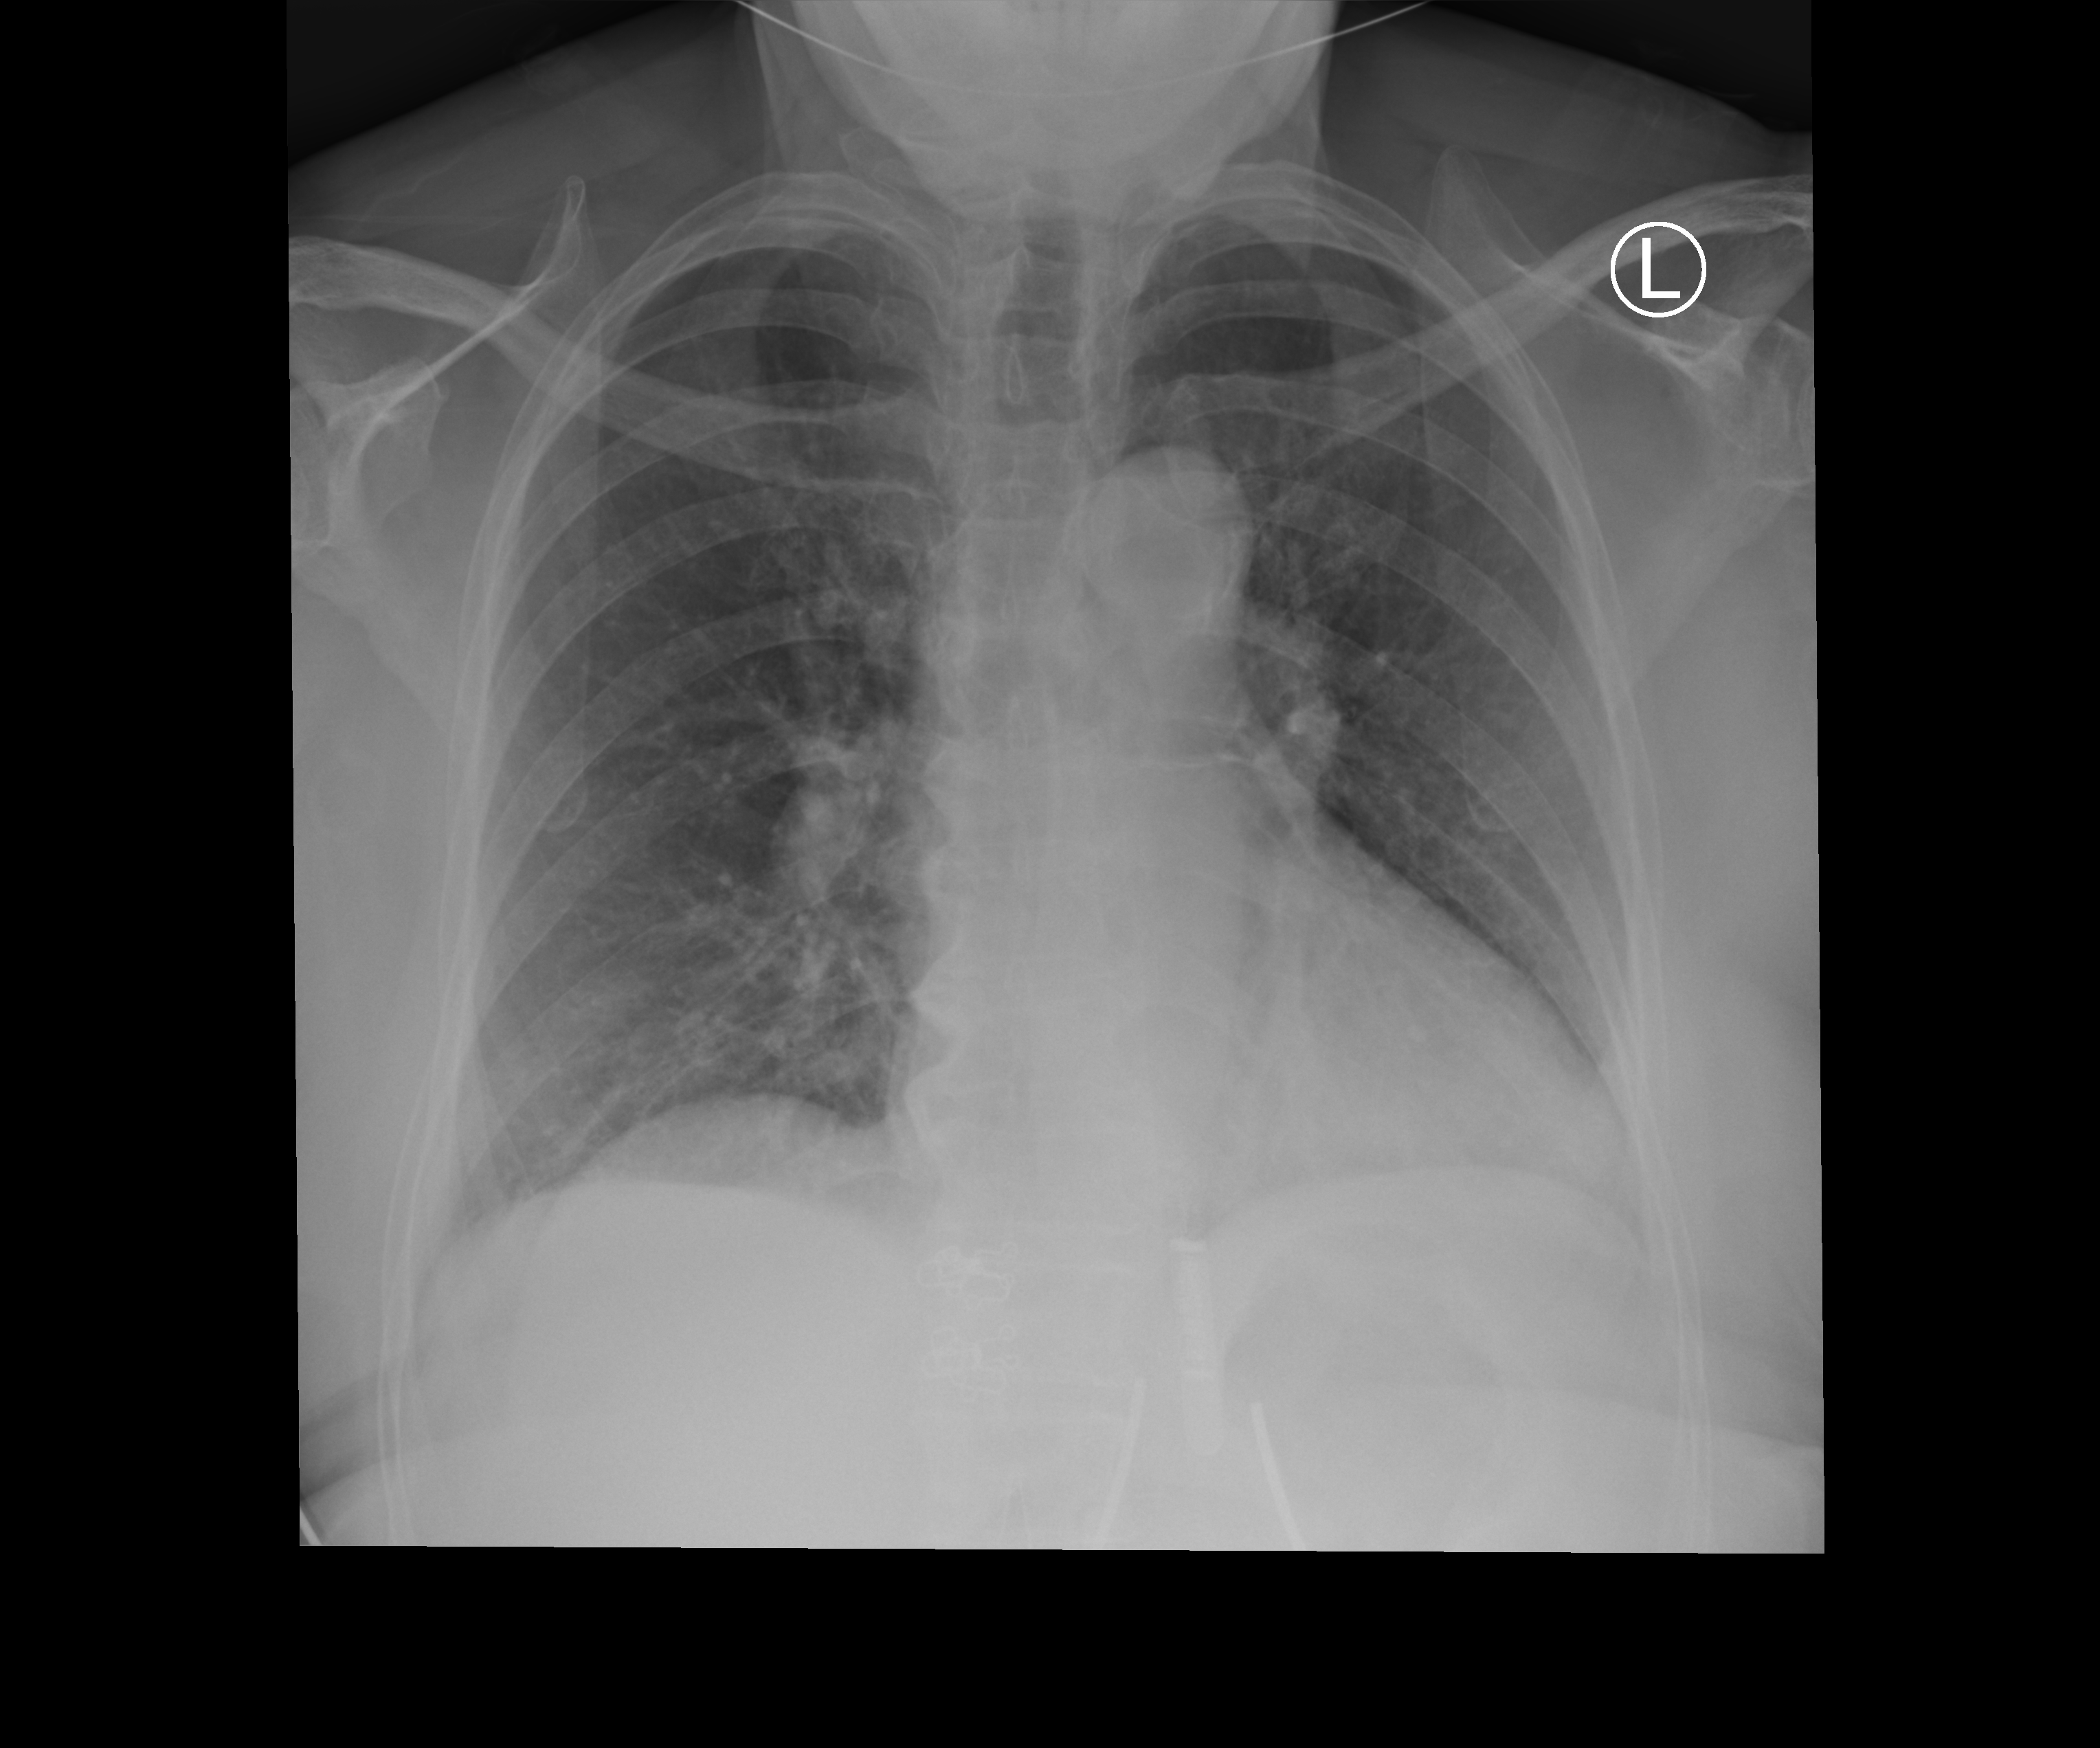
Chest X-ray. Female patient hospitalised with COVID-19, age 75–90 years.
Hospital-stay facts (about this admission, not read from this image; timing relative to this image not recorded):
- mechanically ventilated during this hospital stay: no
- admitted to intensive care during this hospital stay: no